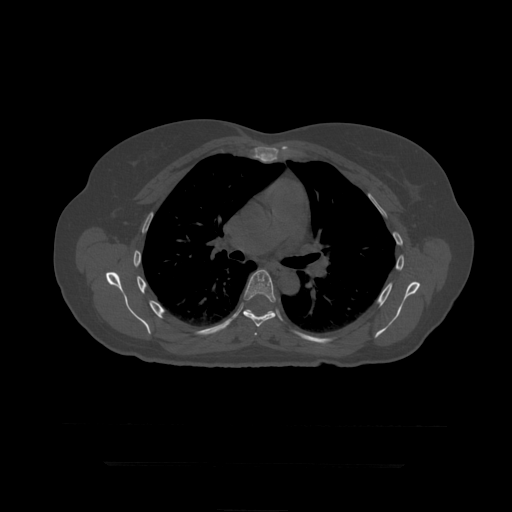
CT including the spine, one axial slice. Slice 299 of 399 in the series (ordered by position). Reconstruction kernel STANDARD. Bone window (W 1800 / L 400 HU). 1.25 mm slice thickness. 512 × 512 image matrix, field of view 450 × 450 mm. Patient age 41 years. Case-level facts recorded for this patient, not image findings: primary cancer: breast.
Structures marked on this image (semi-automatic segmentation, software-assisted and operator-edited):
- T6 vertebra: bounding box (x1, y1, x2, y2) in pixels: (254, 333, 258, 336)
- T7 vertebra: (243, 270, 276, 327)
- T8 vertebra: (251, 311, 272, 312)